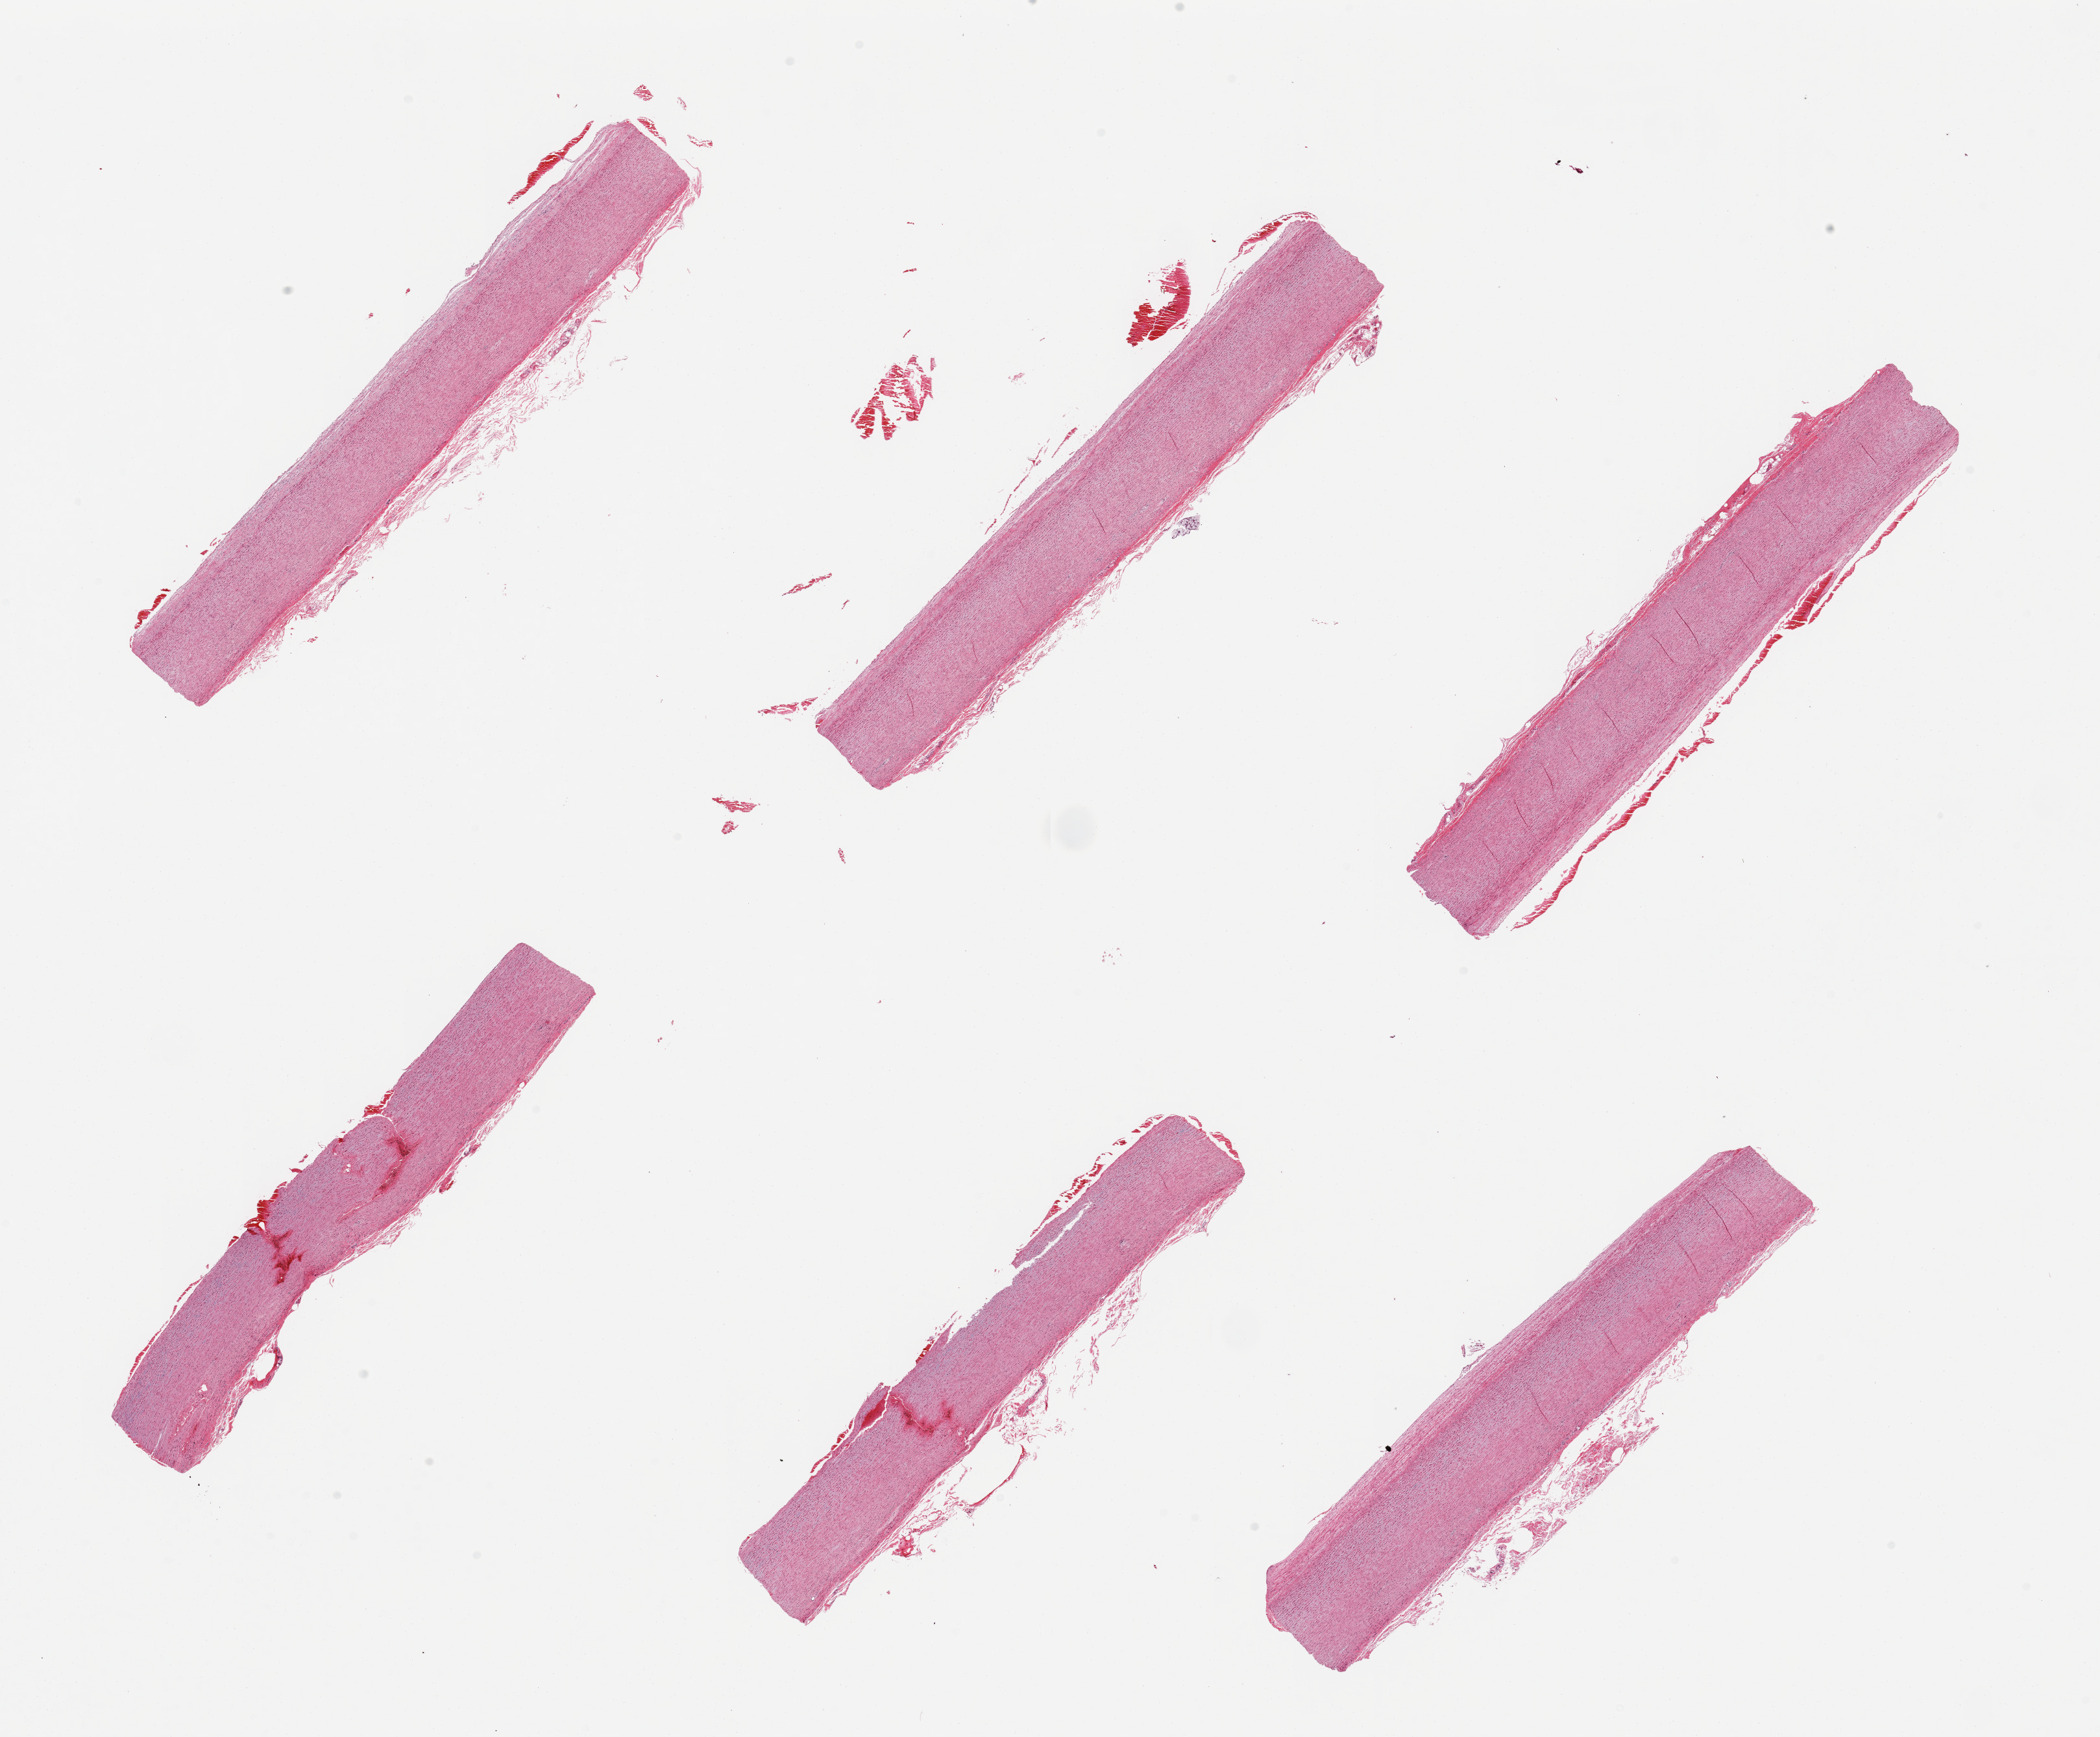
Whole-slide image, haematoxylin and eosin stain, brightfield — shown as a low-resolution overview of the whole scanned area (about 25.6 x 21.2 mm); PAXgene-fixed paraffin-embedded (PFPE) section; section of aorta (target tissue); tissue donor sample. Female donor.
Reviewer comment on this tissue sample: 6 pieces, minimla atherosis.